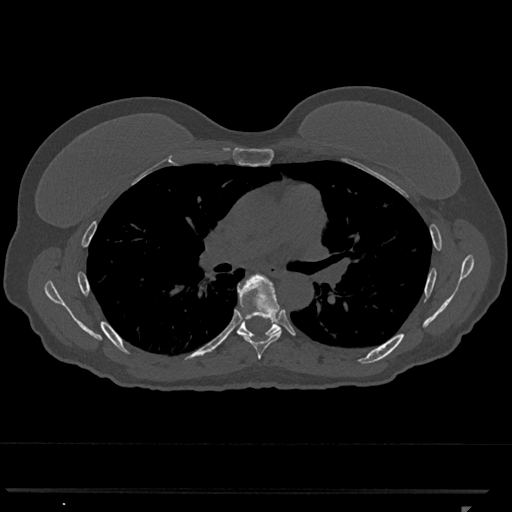
CT including the spine, one axial slice; slice 742 of 793 in the series (ordered by position); 120 kVp; bone window (W 1800 / L 400 HU); 0.5 mm slice thickness; 512 × 512 image matrix, field of view 380 × 380 mm. Female patient, age 62 years. Case-level facts recorded for this patient, not image findings: primary cancer: renal.
Structures marked on this image (semi-automatically segmented with operator editing):
- T6 vertebra: box from (x=237, y=273) to (x=282, y=359) px
- T7 vertebra: (x=236, y=317)–(x=280, y=337)